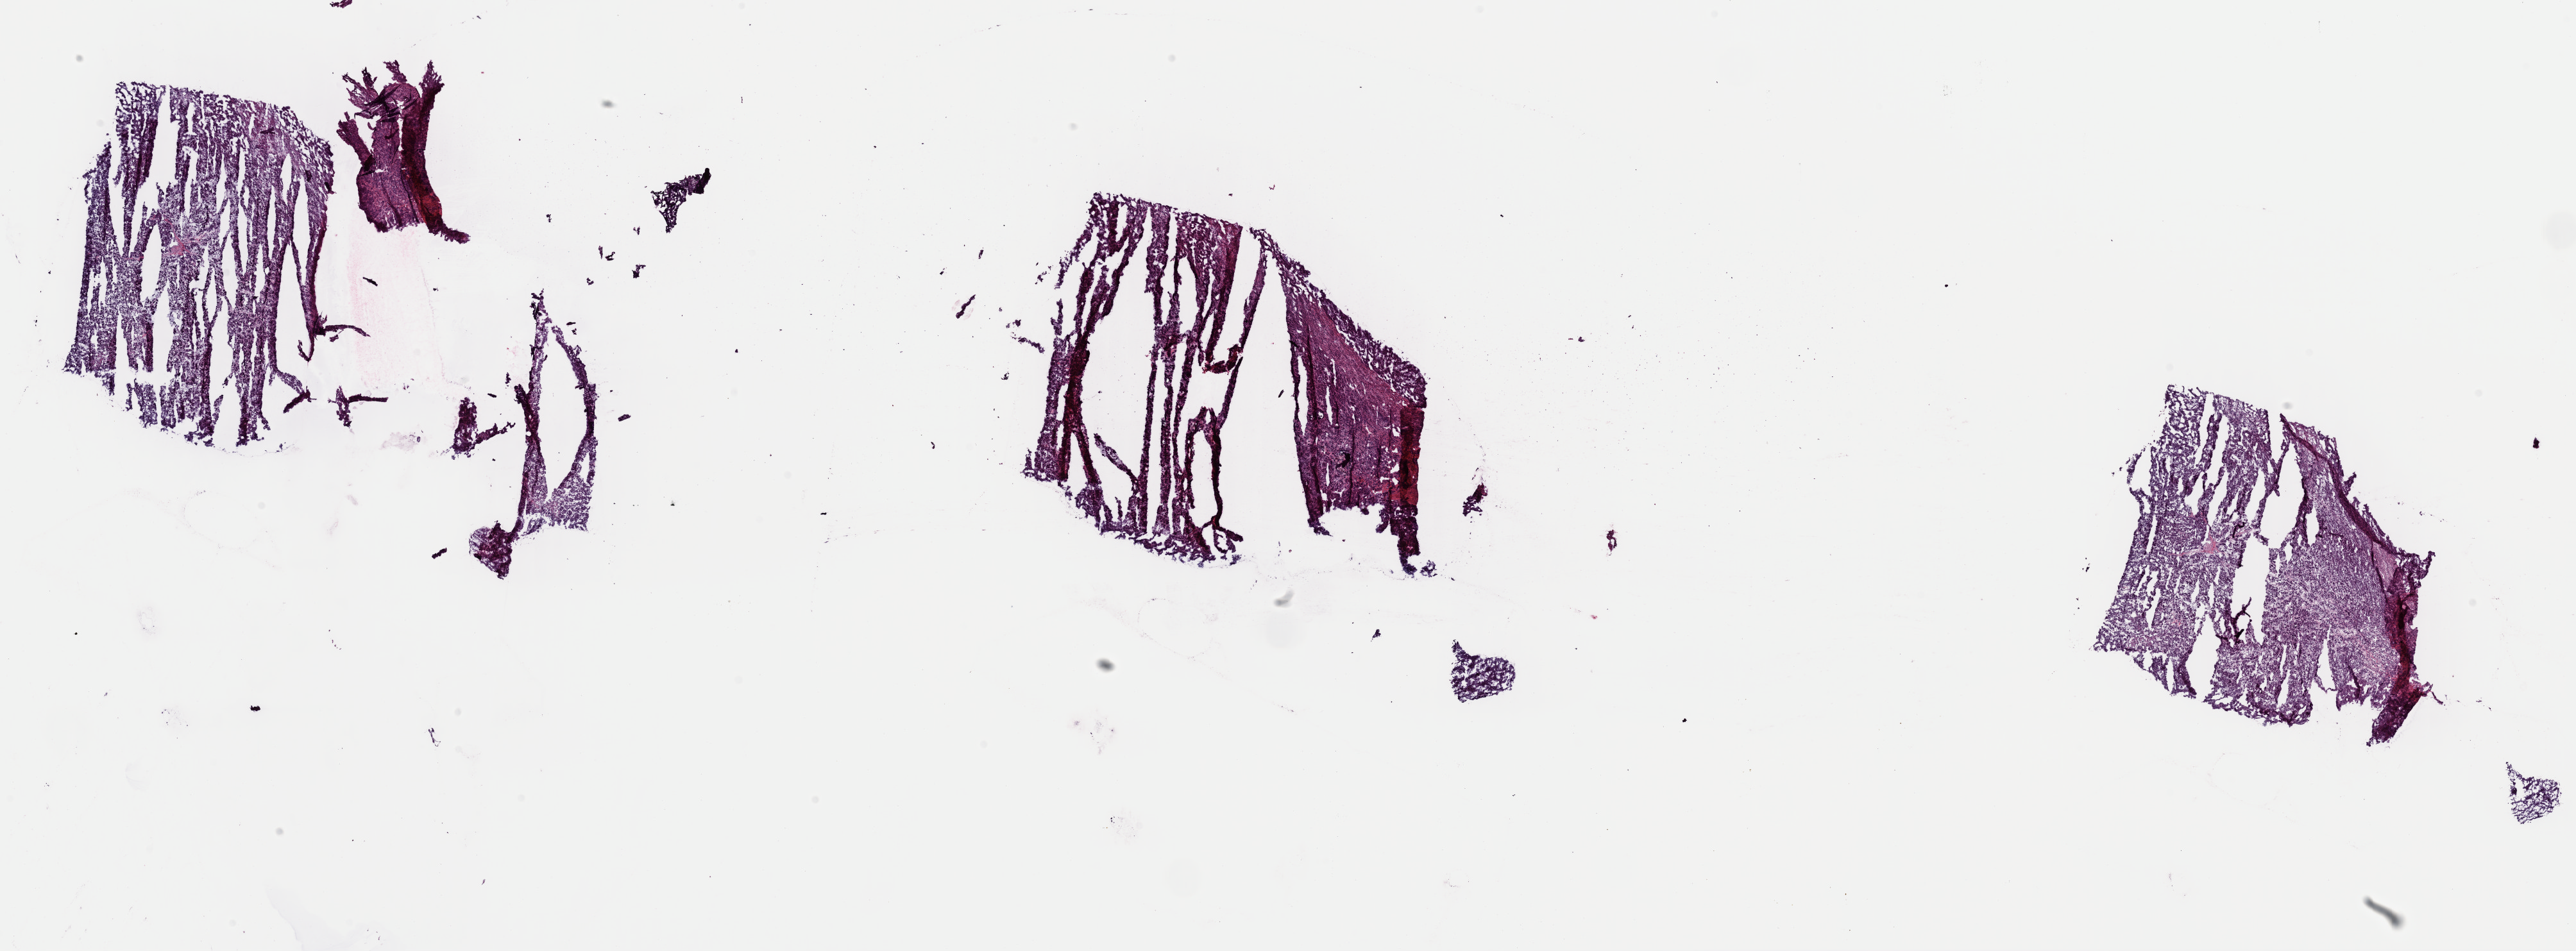
Hematoxylin and eosin (H&E) stained whole-slide image, whole scanned area (about 31.7 x 11.7 mm, from a 40x scan) shown as a low-resolution overview. Frozen section. Adrenal cortex, primary tumour sample. Female patient; age at initial diagnosis 44 years. Slide review estimates, as recorded: tumour cells 95%, tumour nuclei 100%, normal cells 0%, stromal cells 5%, necrosis 0%. Infiltration values recorded for this section: lymphocyte infiltration 0%, monocyte infiltration 0%, neutrophil infiltration 0%.
• diagnosis: Adrenal cortical carcinoma (cortex of adrenal gland)